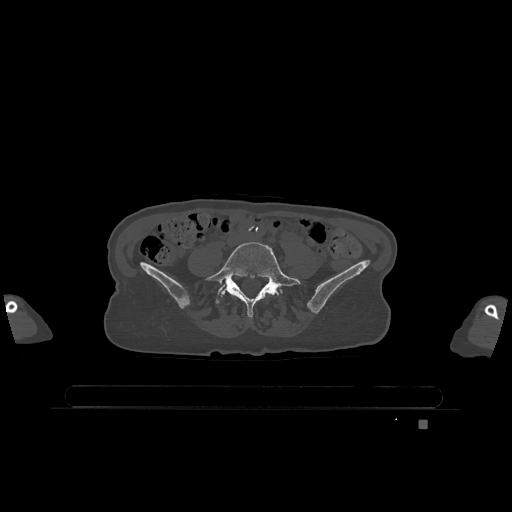
CT including the spine, one axial slice. Position 244 of 1317 along the scan axis. Bone window (W 1800 / L 400 HU). 512 × 512 image matrix. Patient: female, 74 years. From the clinical record (not read from this slice): primary cancer: lung.
Outlined on this slice (semi-automatically segmented with operator editing):
- L5 vertebra: bounding box [x1, y1, x2, y2] px = [205, 242, 301, 317]